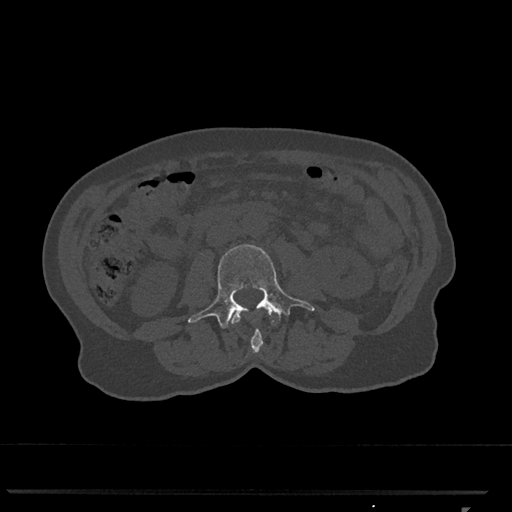
CT including the spine, one axial slice. Reconstruction kernel Br40s/3. 120 kVp. Bone window (W 1800 / L 400 HU). 0.5 mm slice thickness. 512 × 512 image matrix. Patient: female, 62 years. From the clinical record (not read from this slice): primary cancer: renal.
Outlined on this slice (semi-automatic segmentation, software-assisted and operator-edited):
- L2 vertebra: box from (x=231, y=308) to (x=275, y=353) px
- L3 vertebra: (x=188, y=244)–(x=315, y=328)